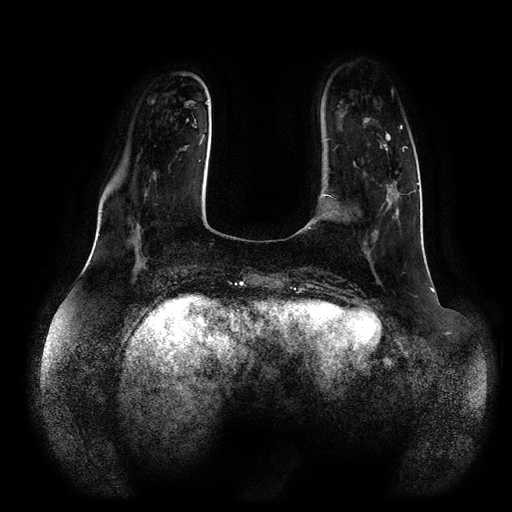
Breast MRI (dynamic contrast-enhanced, multi-phase), one axial slice. Slice 25 of 116 in the series (ordered by position). Dynamic contrast-enhanced series, time point 2 of 5 at this slice position (early post-contrast). 1.5 T. TE 2.5 ms, TR 5.2 ms. 2 mm slice thickness. 512 × 512 image matrix, field of view 400 × 400 mm. Female patient, age 66 years.
Outlined on this slice (semi-automatic segmentation, software-assisted and operator-edited):
- breast lesion (labelled 'tumour' in the annotation; benign lesions carry a separate 'benign' label): bounding box (x1, y1, x2, y2) in pixels: (364, 118, 401, 246)